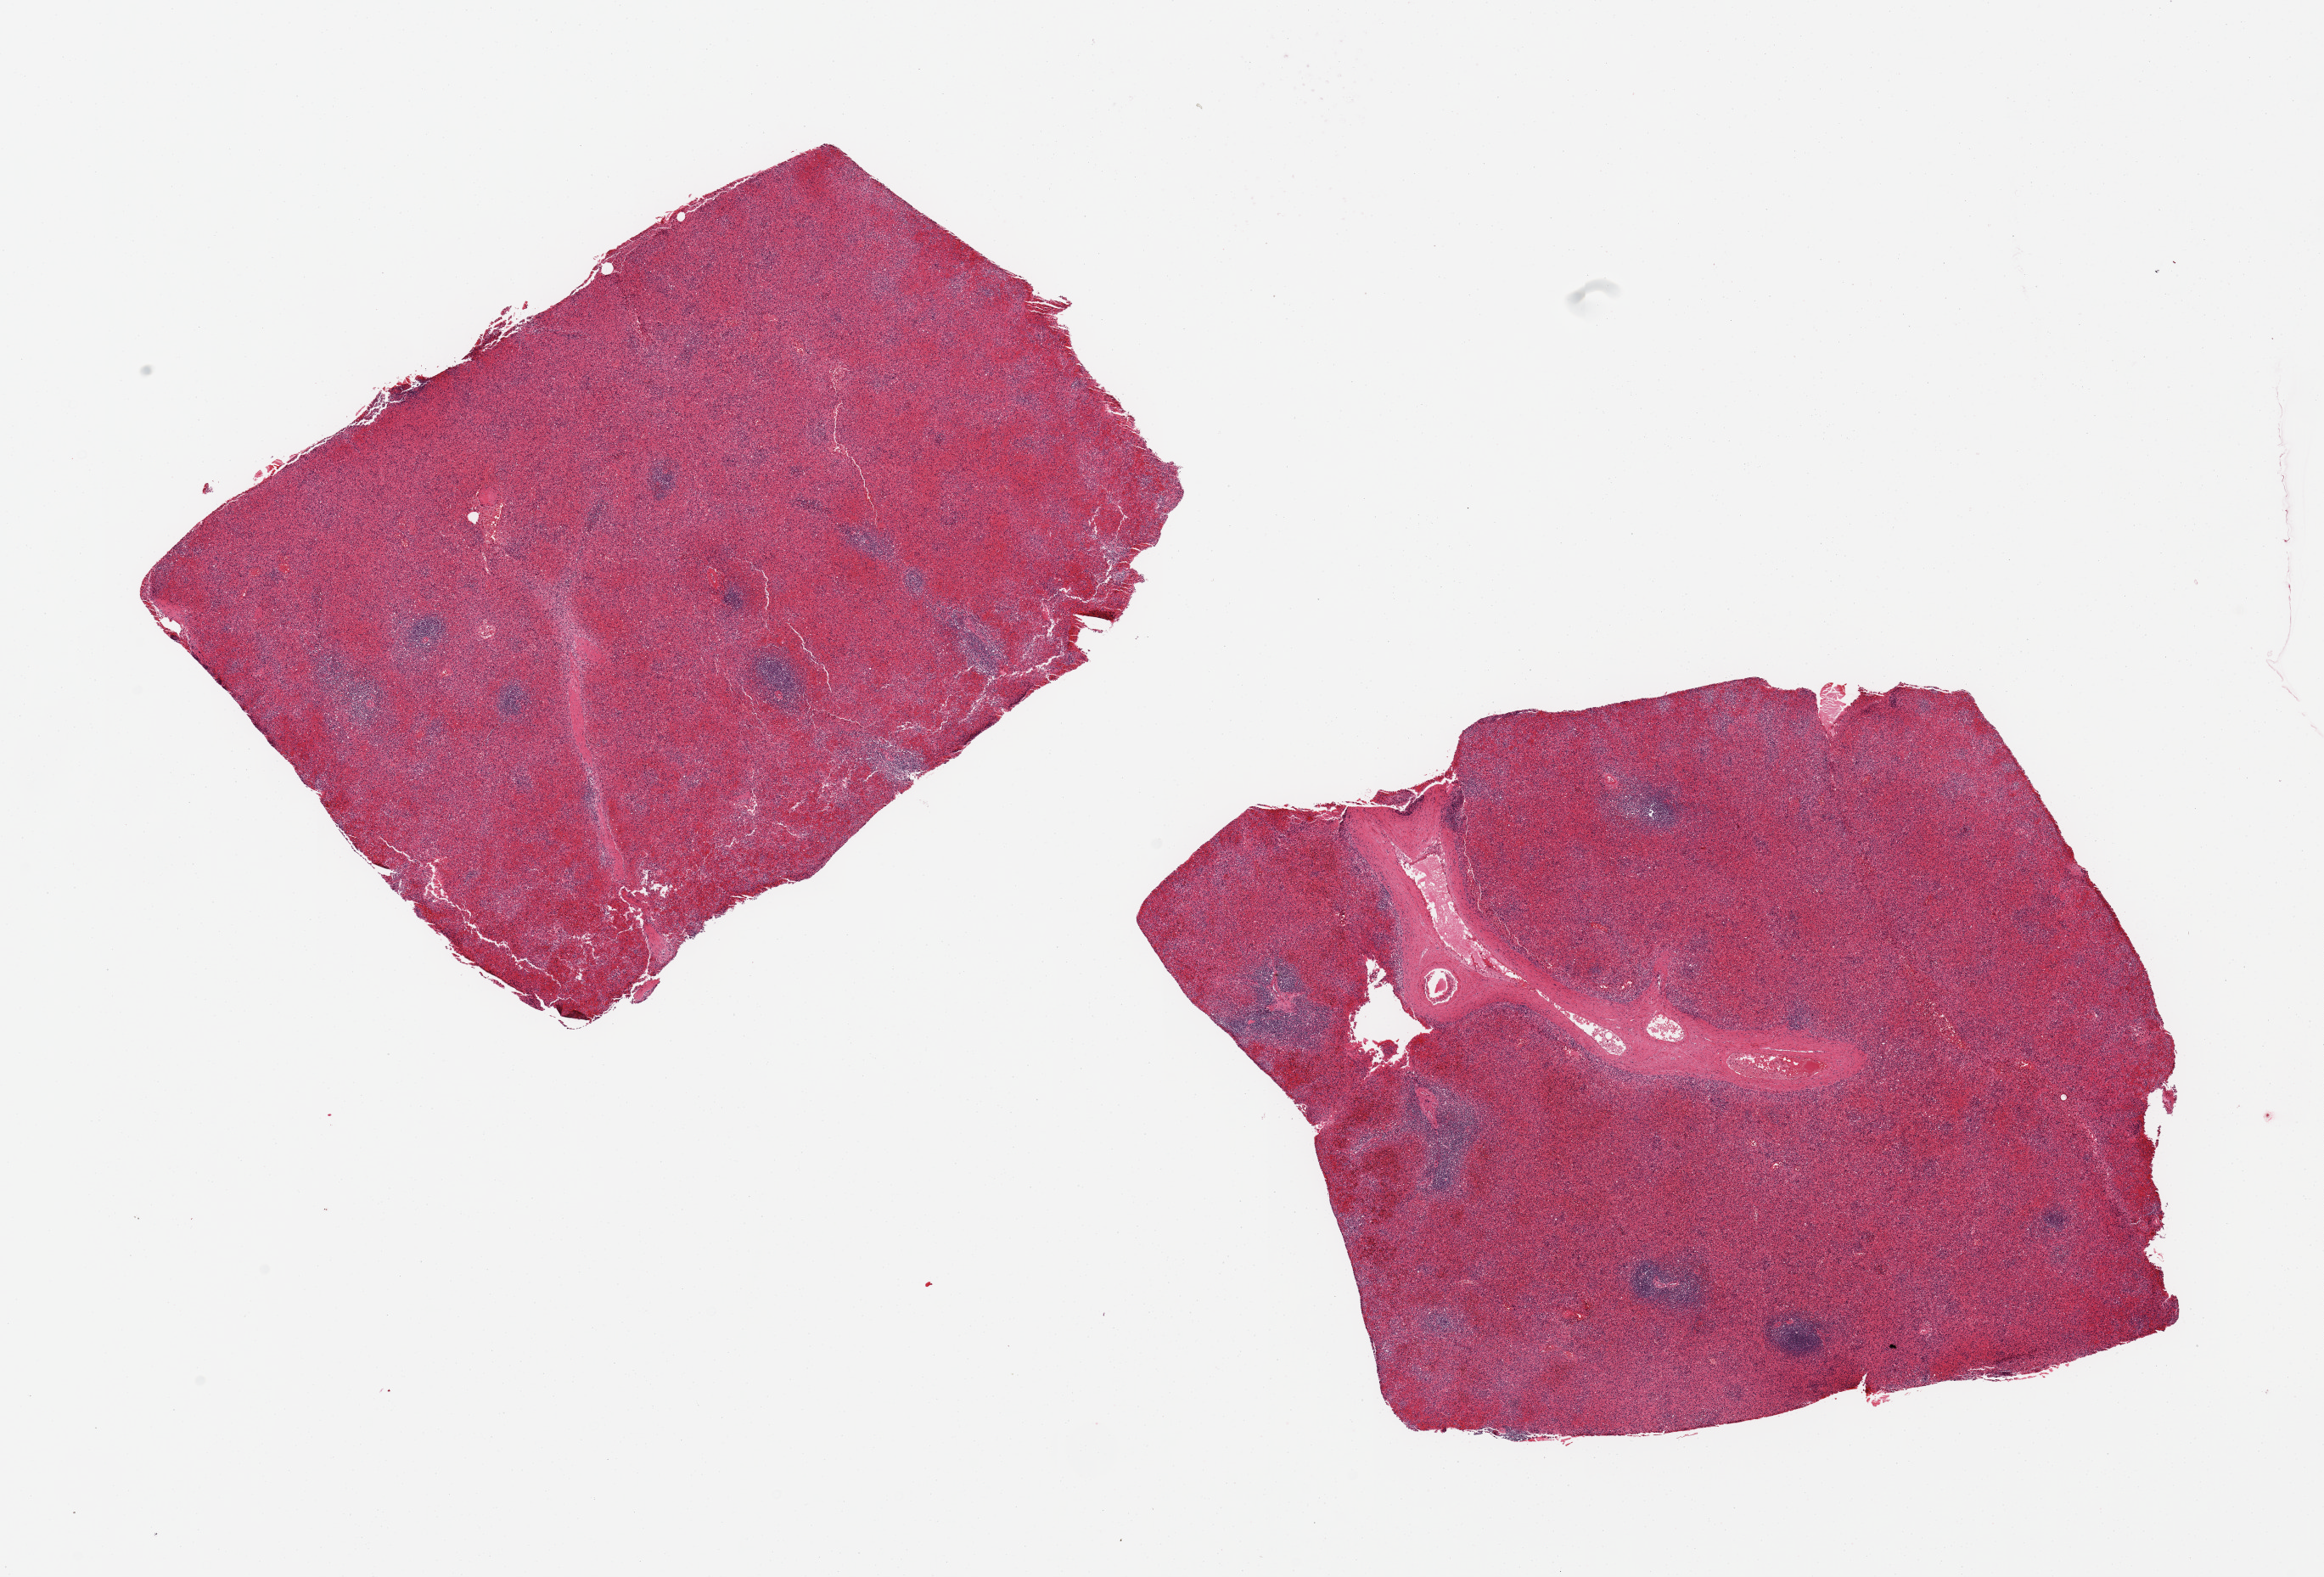
Whole-slide image, H&E stain — low-resolution overview of the scanned area, about 21.7 x 14.7 mm (slide scanned at 20x); PAXgene-fixed, paraffin-embedded tissue; target tissue: spleen; tissue donor sample. Donor: male.
Pathologist's review note for this sample: 2 pieces; moderately congested.